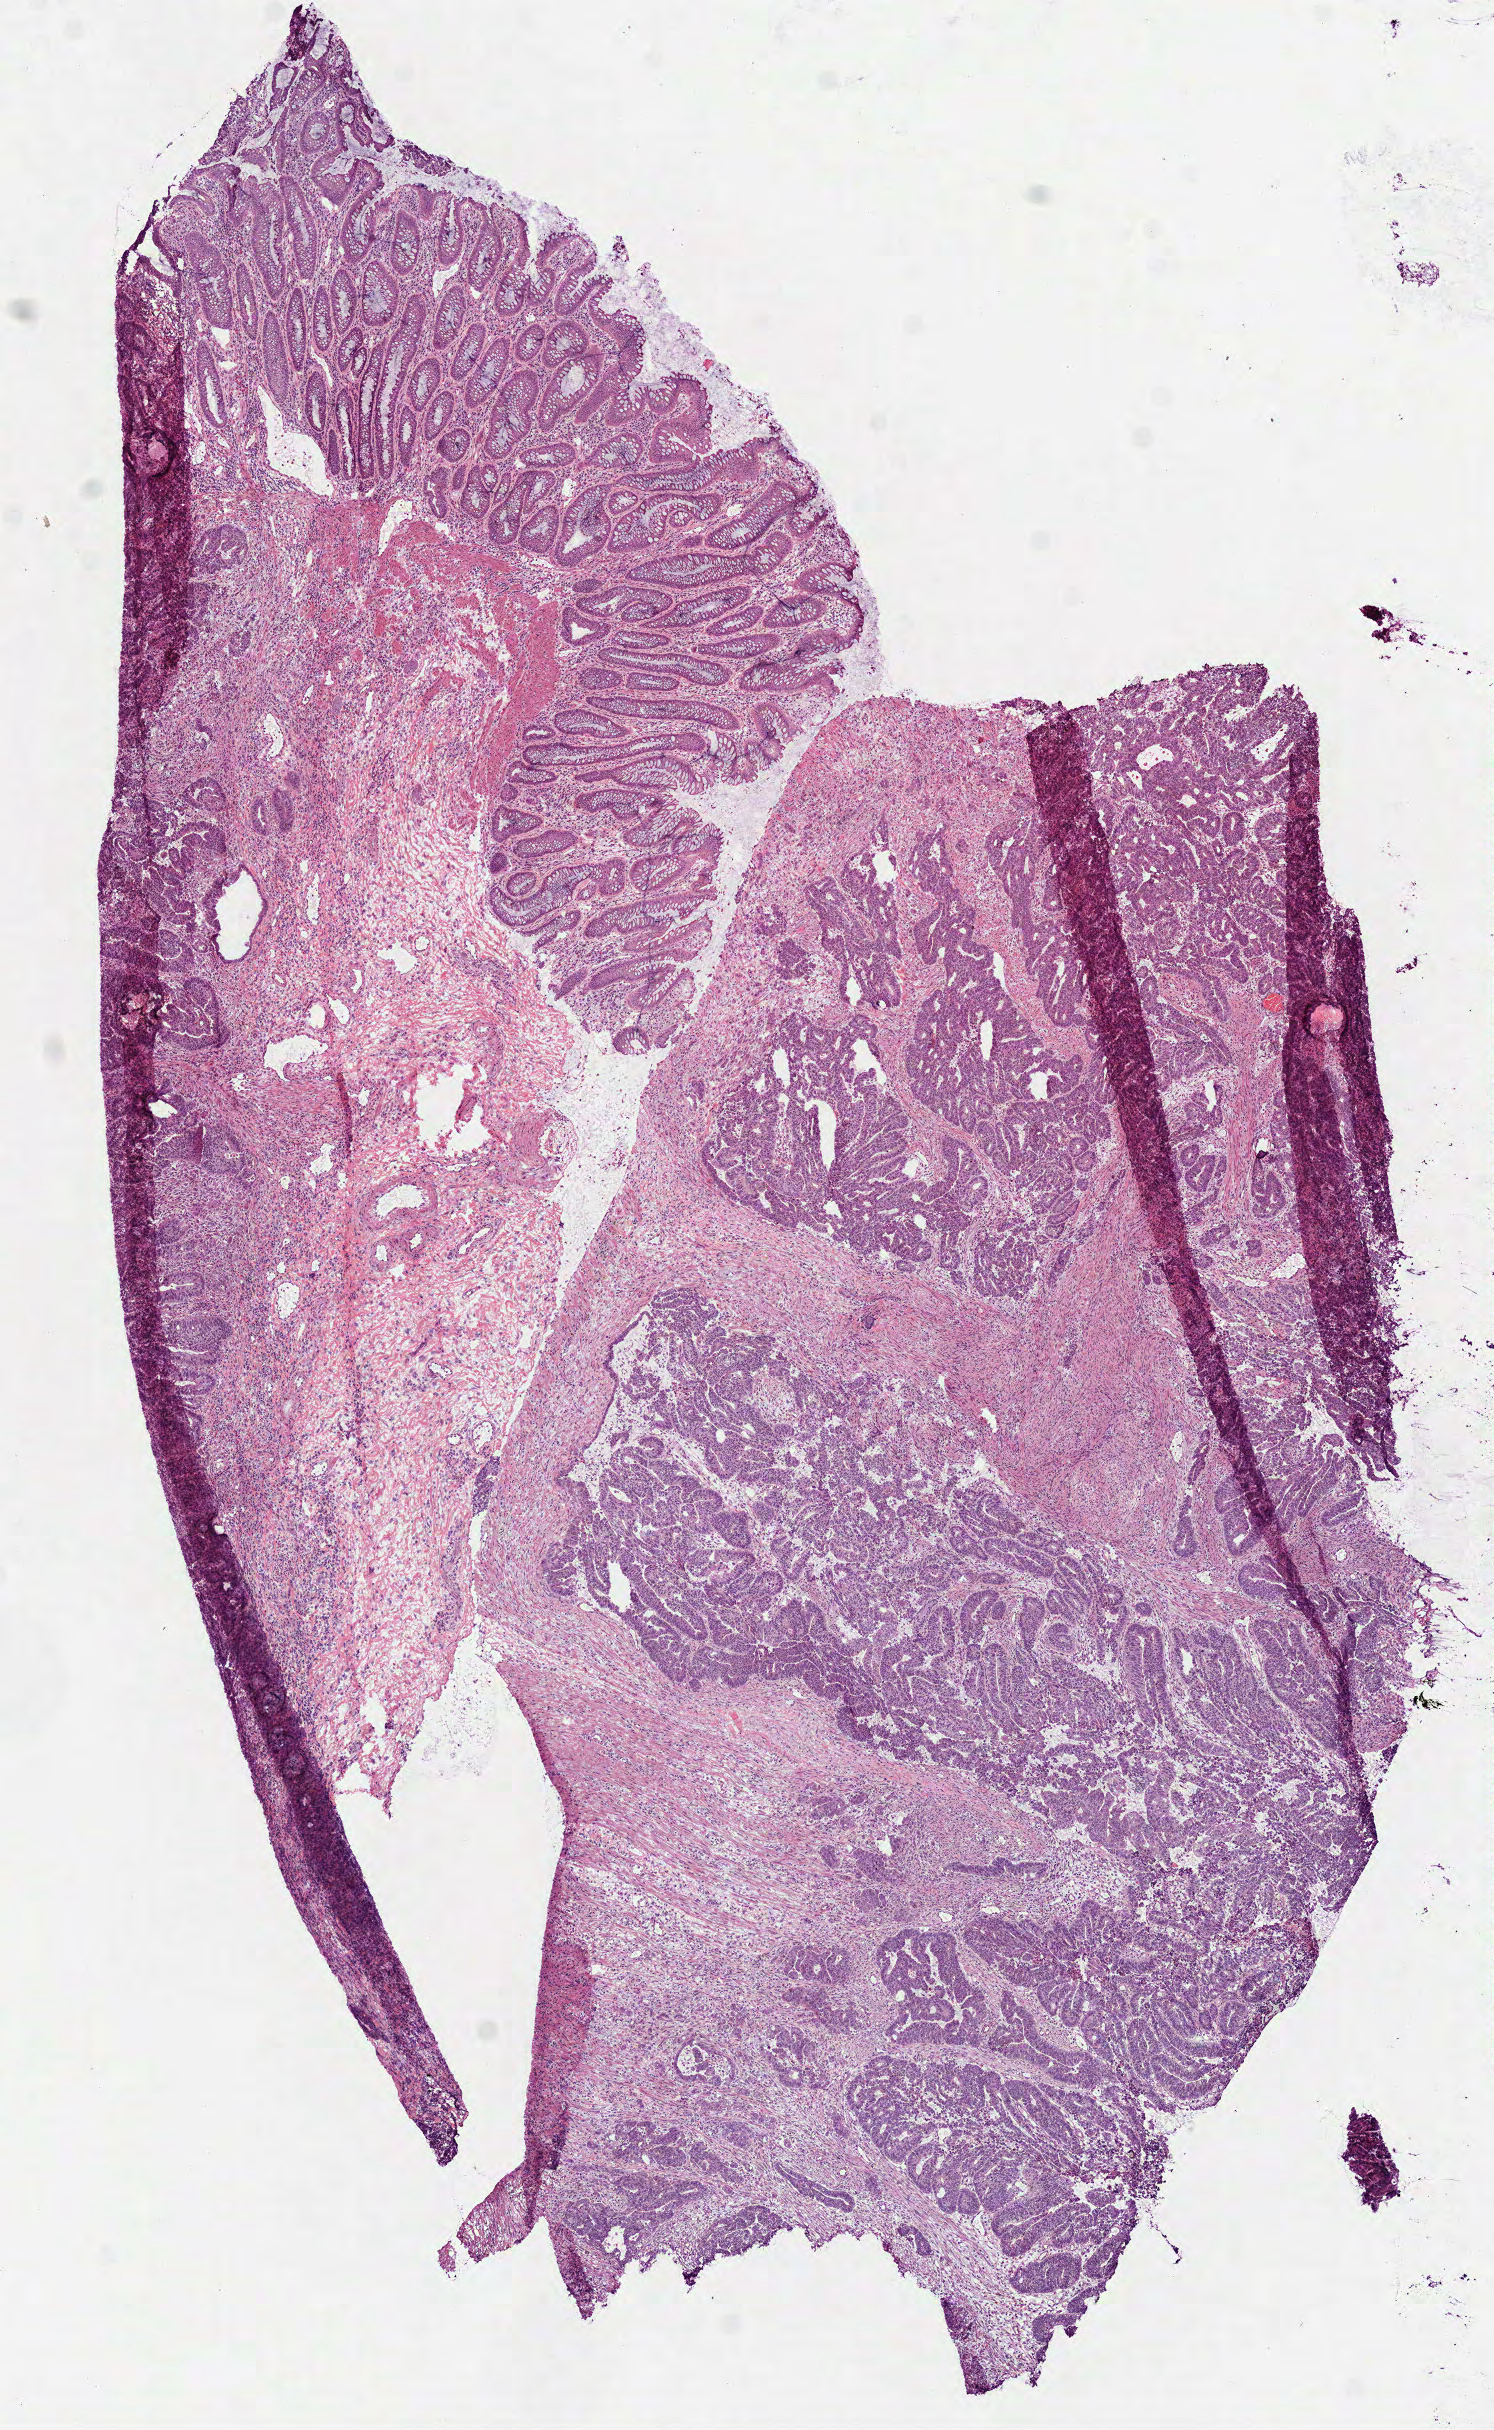
Whole-slide histology image, H&E — a low-resolution overview of the entire scanned area, about 6.0 x 9.8 mm, frozen section from the bottom of the tissue portion, rectum, primary tumour sample. Male patient; age at initial diagnosis 66 years. Pathologist review of this section (percent, as recorded): tumour cells 69%, tumour nuclei 55%, normal cells 20%, stromal cells 10%, necrosis 1%. Inflammatory infiltration, as recorded: lymphocyte infiltration 15%, monocyte infiltration 5%, neutrophil infiltration 15%.
• AJCC pathologic stage: IIIA (7th edition)
• pathologic diagnosis: Adenocarcinoma, NOS (rectosigmoid junction)